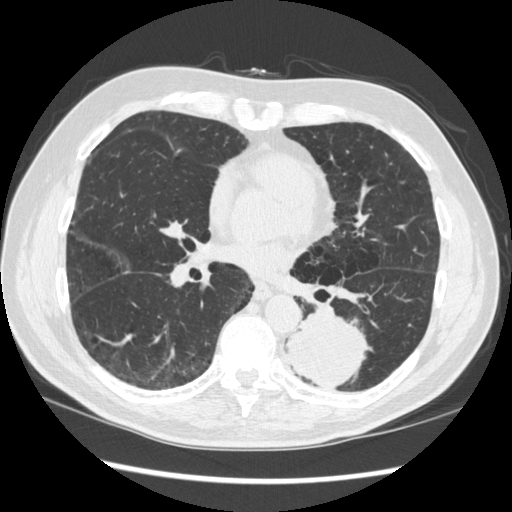
Low-dose screening chest CT, one axial slice. Slice 152 of 348 in the series (ordered by position). 120 kVp. Lung window (W 1500 / L -600 HU). 512 × 512 image matrix, field of view 360 × 360 mm.
Annotated regions visible in this slice (expert manual segmentation):
- lesion 1 (tumor, lower lobe of left lung): box from (x=285, y=313) to (x=366, y=390) px